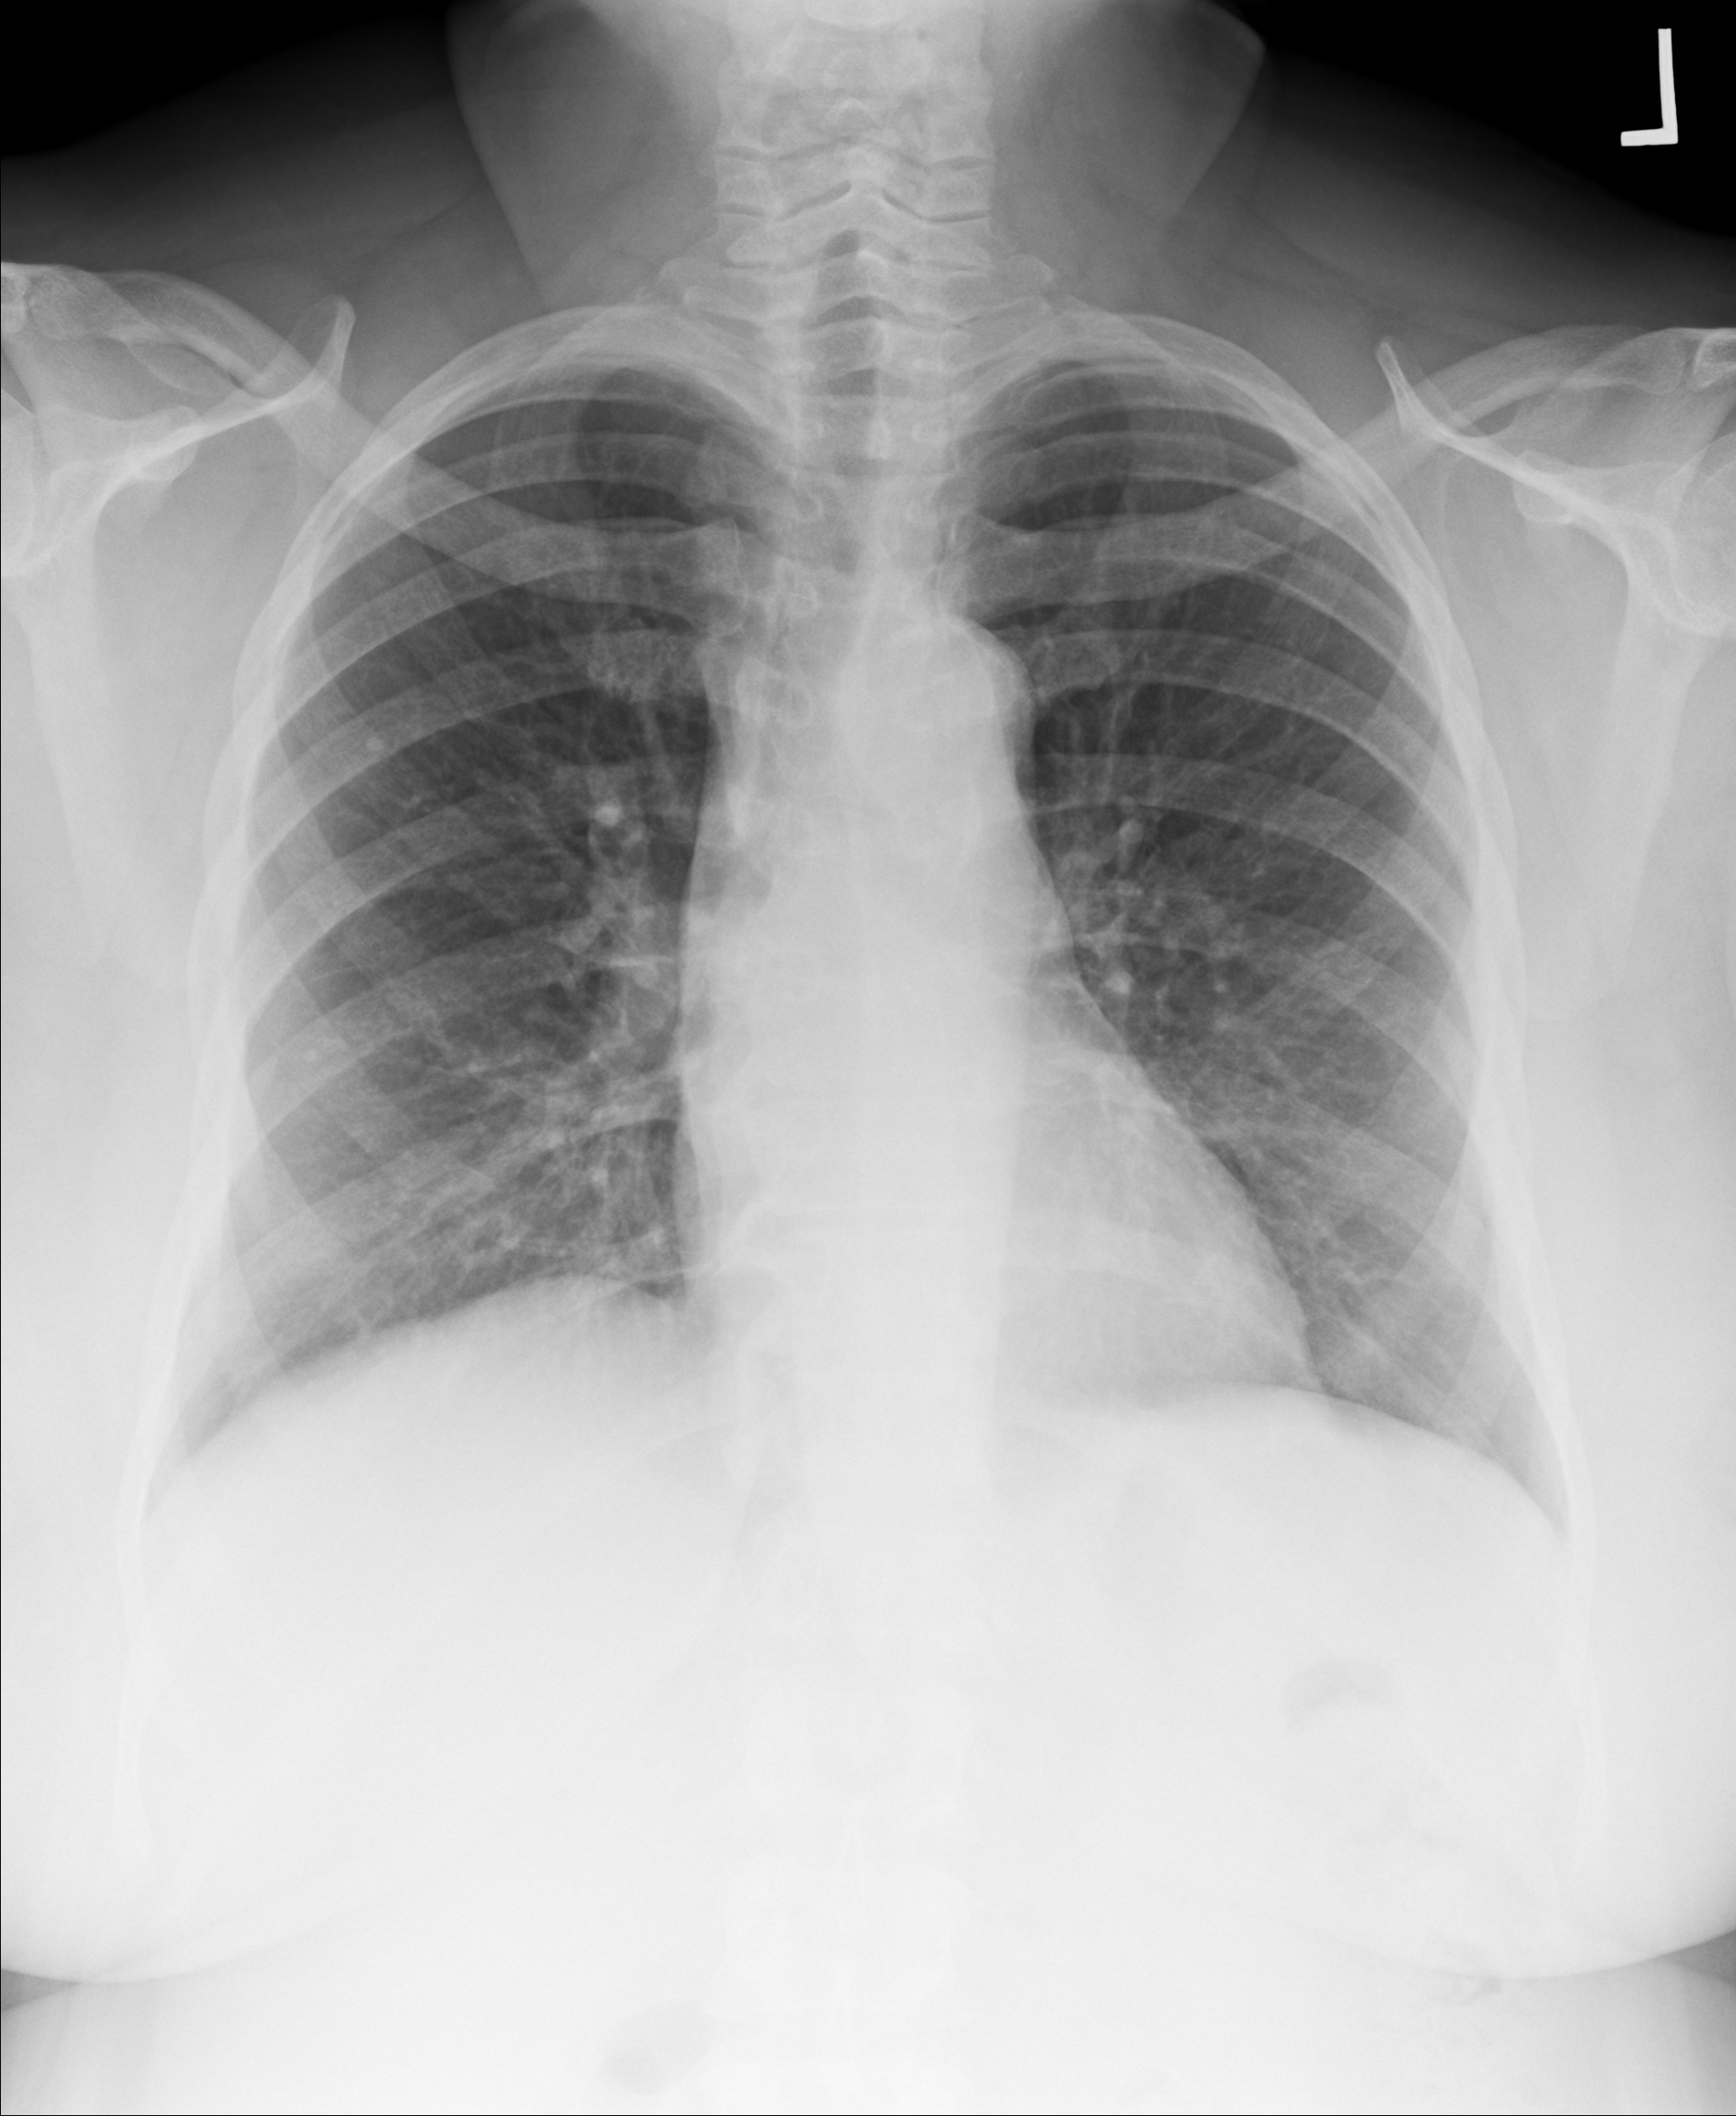
Chest X-ray. Female patient, age 61 years; imaged 51 days after the COVID-19 diagnosis.
Radiologist's key findings for this exam: clearing of previous ill-defined opacities at lung base.